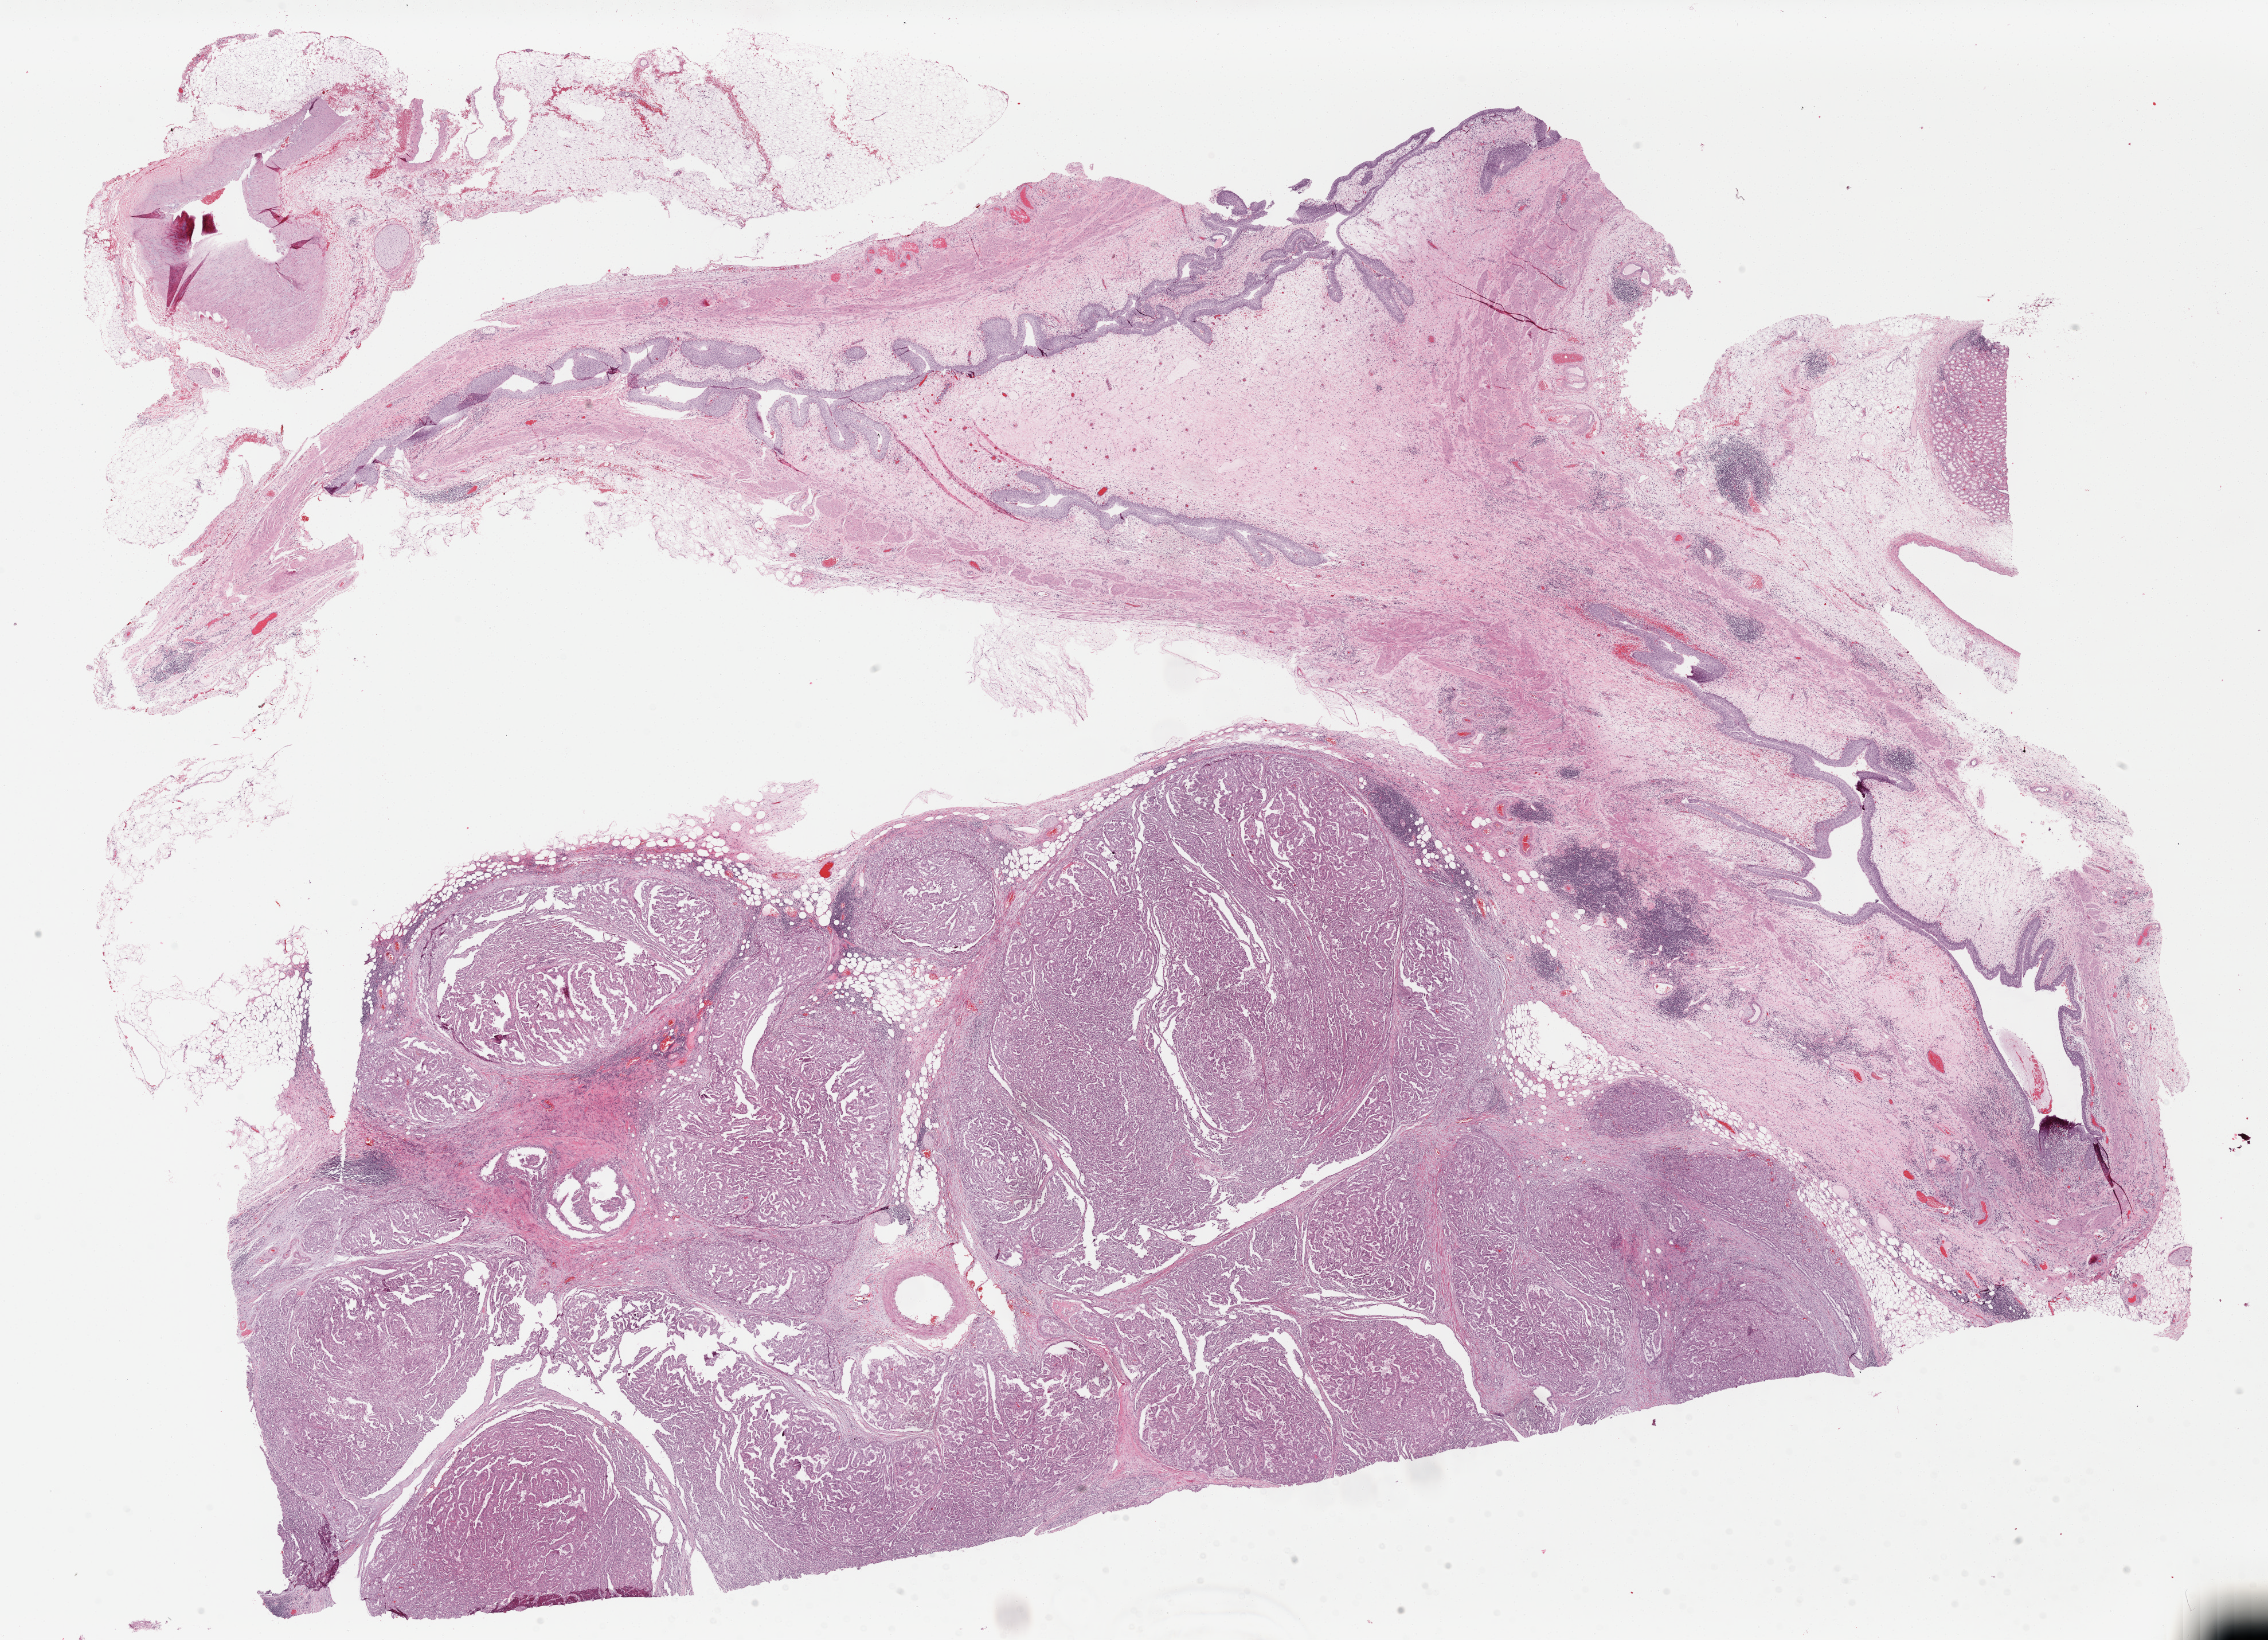
Digitized H&E-stained tissue section (whole slide) — shown as a low-resolution overview of the whole scanned area (about 31.2 x 22.6 mm). Formalin-fixed paraffin-embedded (FFPE) diagnostic section. Kidney, primary tumour sample. Female patient; age at initial diagnosis 61 years.
Diagnosis: Papillary adenocarcinoma, NOS. TNM: T3a NX MX. AJCC pathologic stage: III.